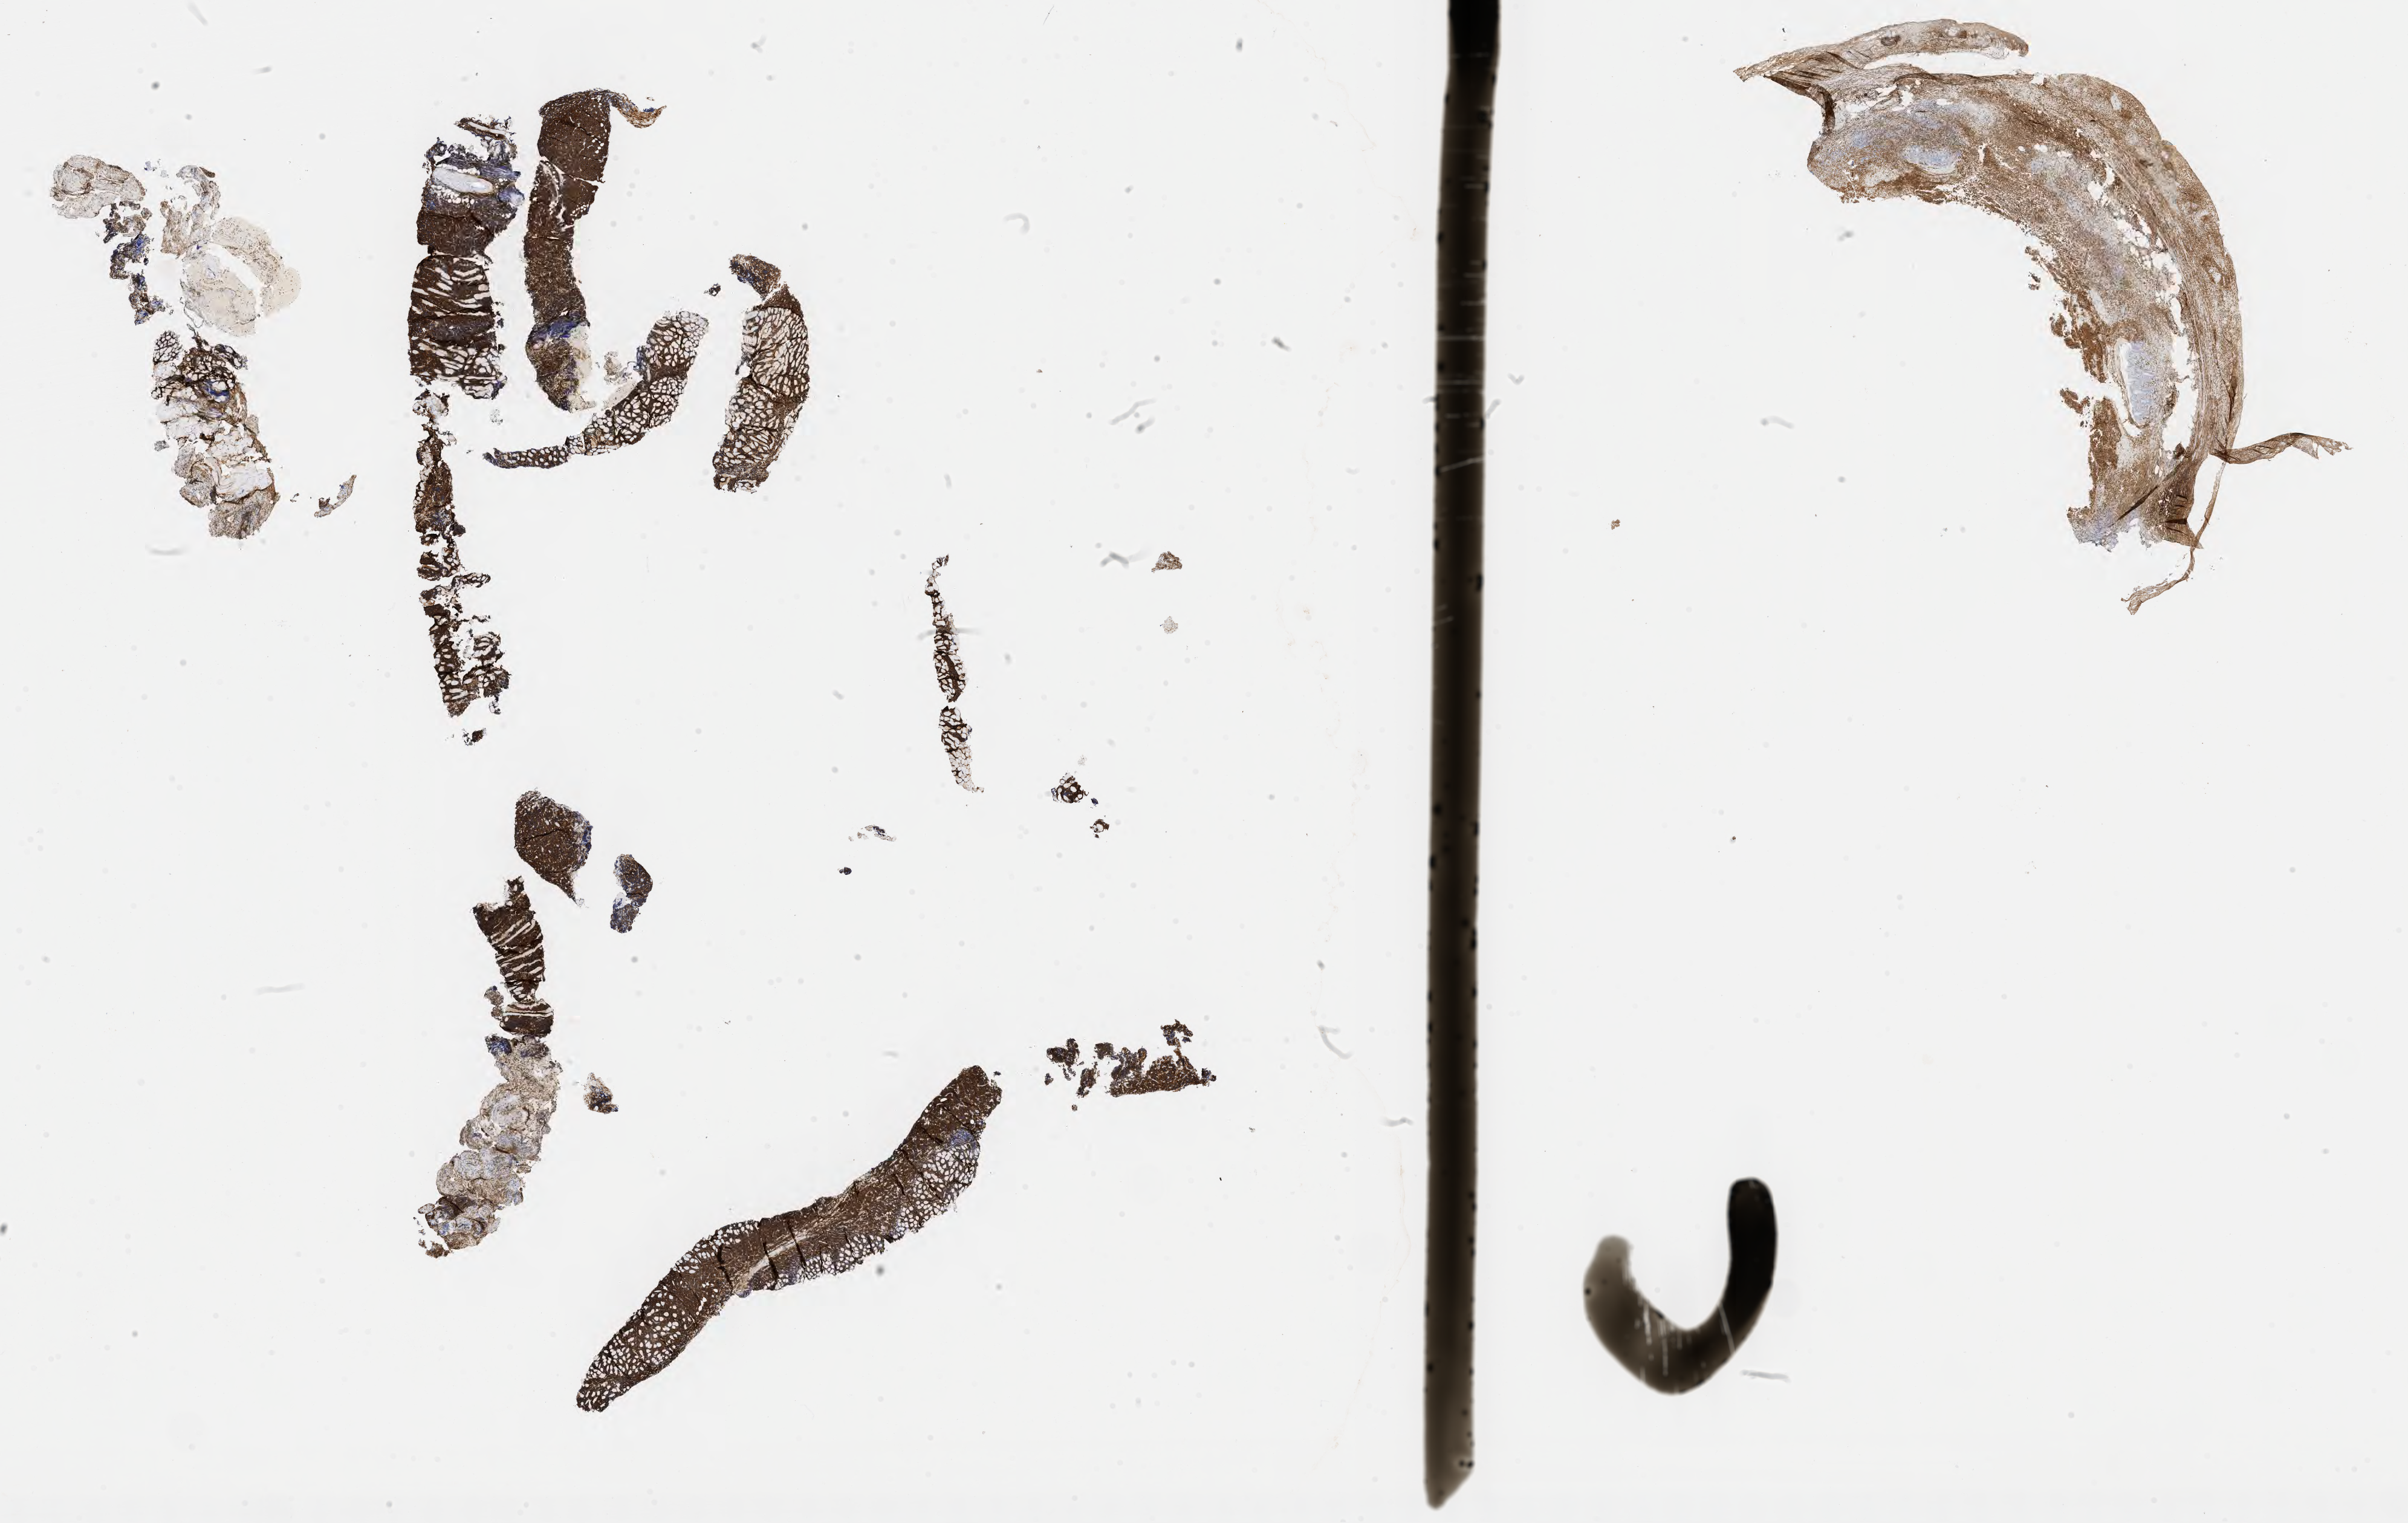
Immunohistochemistry (IHC) whole-slide image stained for CD10, low-resolution overview of the scanned area, about 32.2 x 20.4 mm, specimen: tumor tissue, anatomic site: bone of pelvis. Patient male; age 53 years.
• histologic diagnosis: Burkitt lymphoma, NOS